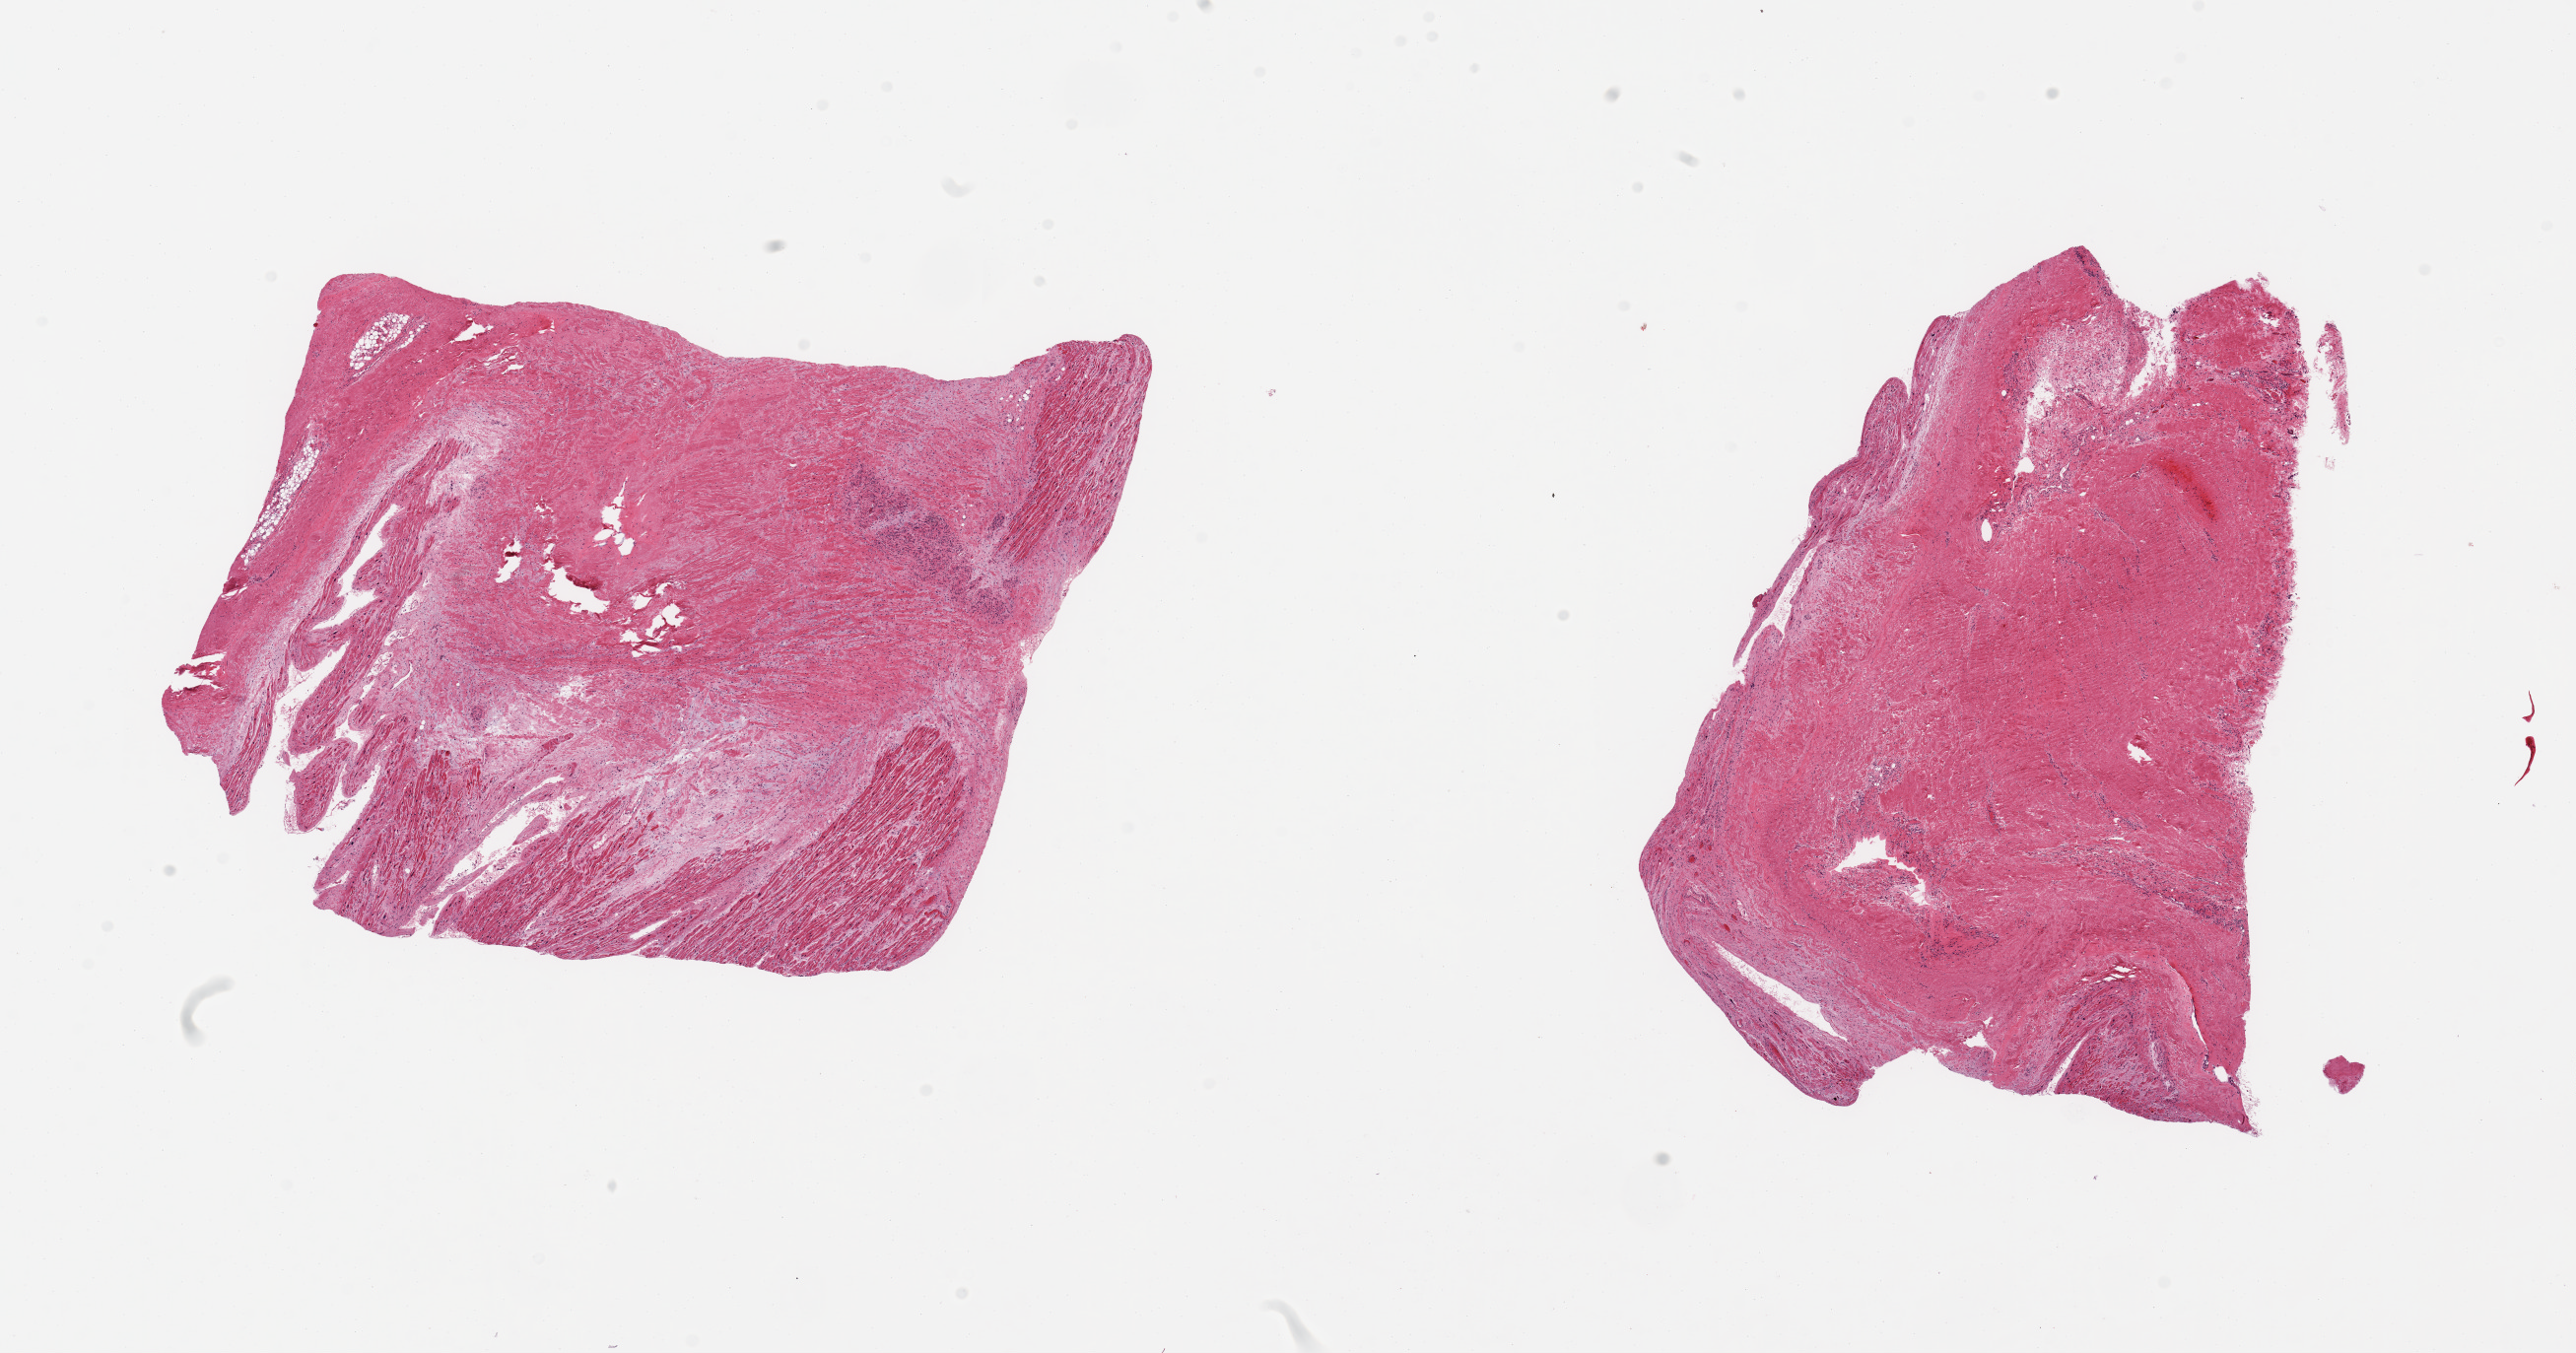
Whole-slide image, H&E stain, a low-resolution overview of the entire scanned area, about 20.7 x 10.9 mm, PAXgene-fixed paraffin-embedded (PFPE) section, sampled site (target tissue): auricular appendage, tissue donor sample. Donor sex: female.
Reviewer comment on this tissue sample: 2 pieces, no abnormalities.